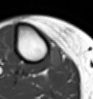
MRI of an extremity soft-tissue mass, one axial slice. Position 35 of 54 along the scan axis. MR volume resampled by the dataset authors to the PET/CT grid (not the native acquisition matrix). 3.27 mm slice thickness. 93 × 99 image matrix, field of view 91 × 97 mm. Female patient. From the clinical record (not read from this slice): histological type: undifferentiated – high grade; grade: high; site of the primary tumour: right thigh.
Outlined on this slice (expert contour drawn on MRI and transferred to this co-registered scan by the dataset authors):
- gross tumour volume (mass): bounding box <47,45,64,69> (left, top, right, bottom; pixels)